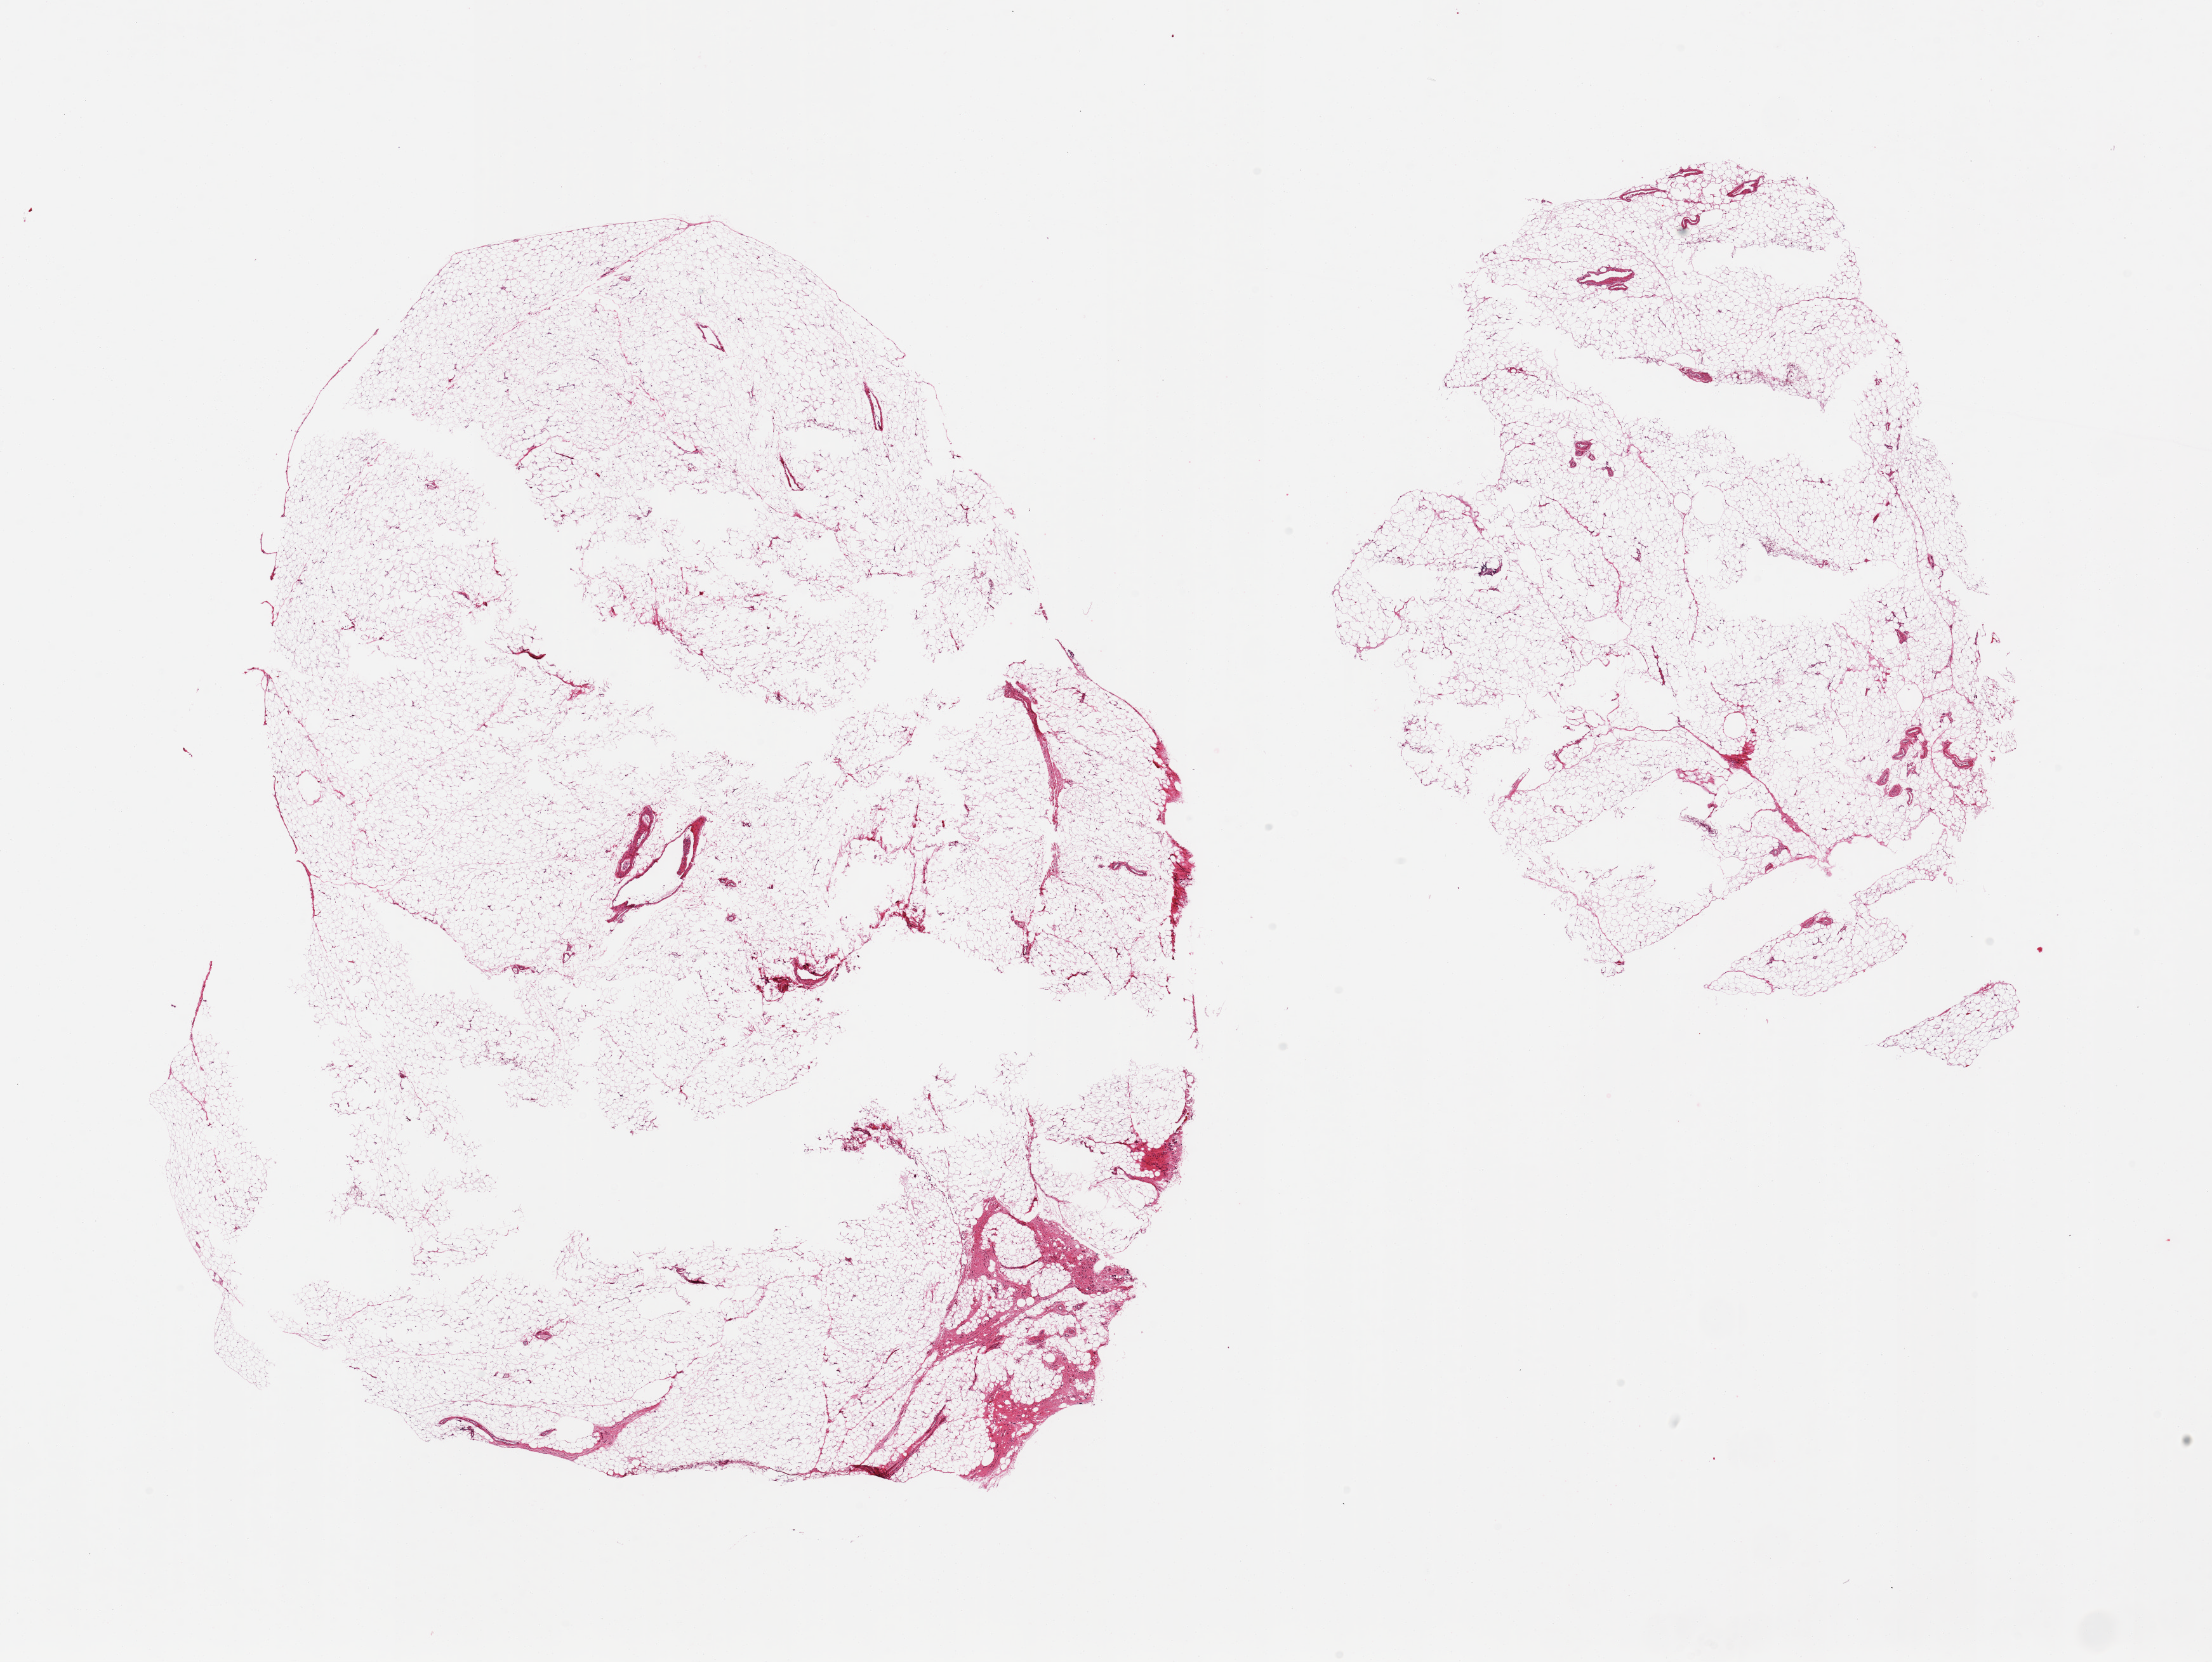
Digitized H&E-stained section — shown as a low-resolution overview of the whole scanned area (about 27.6 x 20.7 mm). PAXgene-fixed paraffin-embedded (PFPE) section. Sampled site (target tissue): omentum. Tissue donor sample. Female donor.
Pathologist's review note for this sample: 2 pieces, trace fascia/vascular elements.